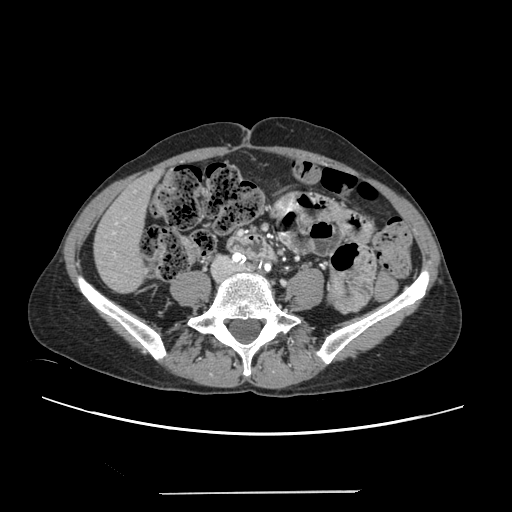
Contrast-enhanced abdominal CT, one axial slice. Position 36 of 240 along the scan axis. Intravenous contrast given. Soft-tissue window (W 400 / L 40 HU). 1.25 mm slice thickness. 512 × 512 image matrix, field of view 371 × 371 mm. Female patient, age 60 years. Case-level facts recorded for this patient, not image findings: diagnosis: colorectal cancer liver metastases, imaged before liver resection.
Outlined on this slice (manually delineated by an expert):
- liver: bounding box <95,175,156,292> (left, top, right, bottom; pixels)
- planned liver remnant (the part of the liver to remain after resection): <95,175,156,292>
- portal vein (with intrahepatic branches): <113,217,126,256>